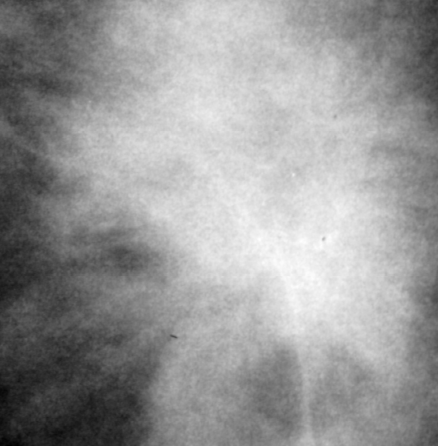
Crop from a digitized film mammogram around one marked abnormality, left breast, CC view, BI-RADS breast density category 3 (scale 1–4).
Mass, shape irregular, margins spiculated; BI-RADS assessment category 5; subtlety rating 5 on a 1 (subtle) to 5 (obvious) scale; pathology result (as recorded, not read from the image): malignant.